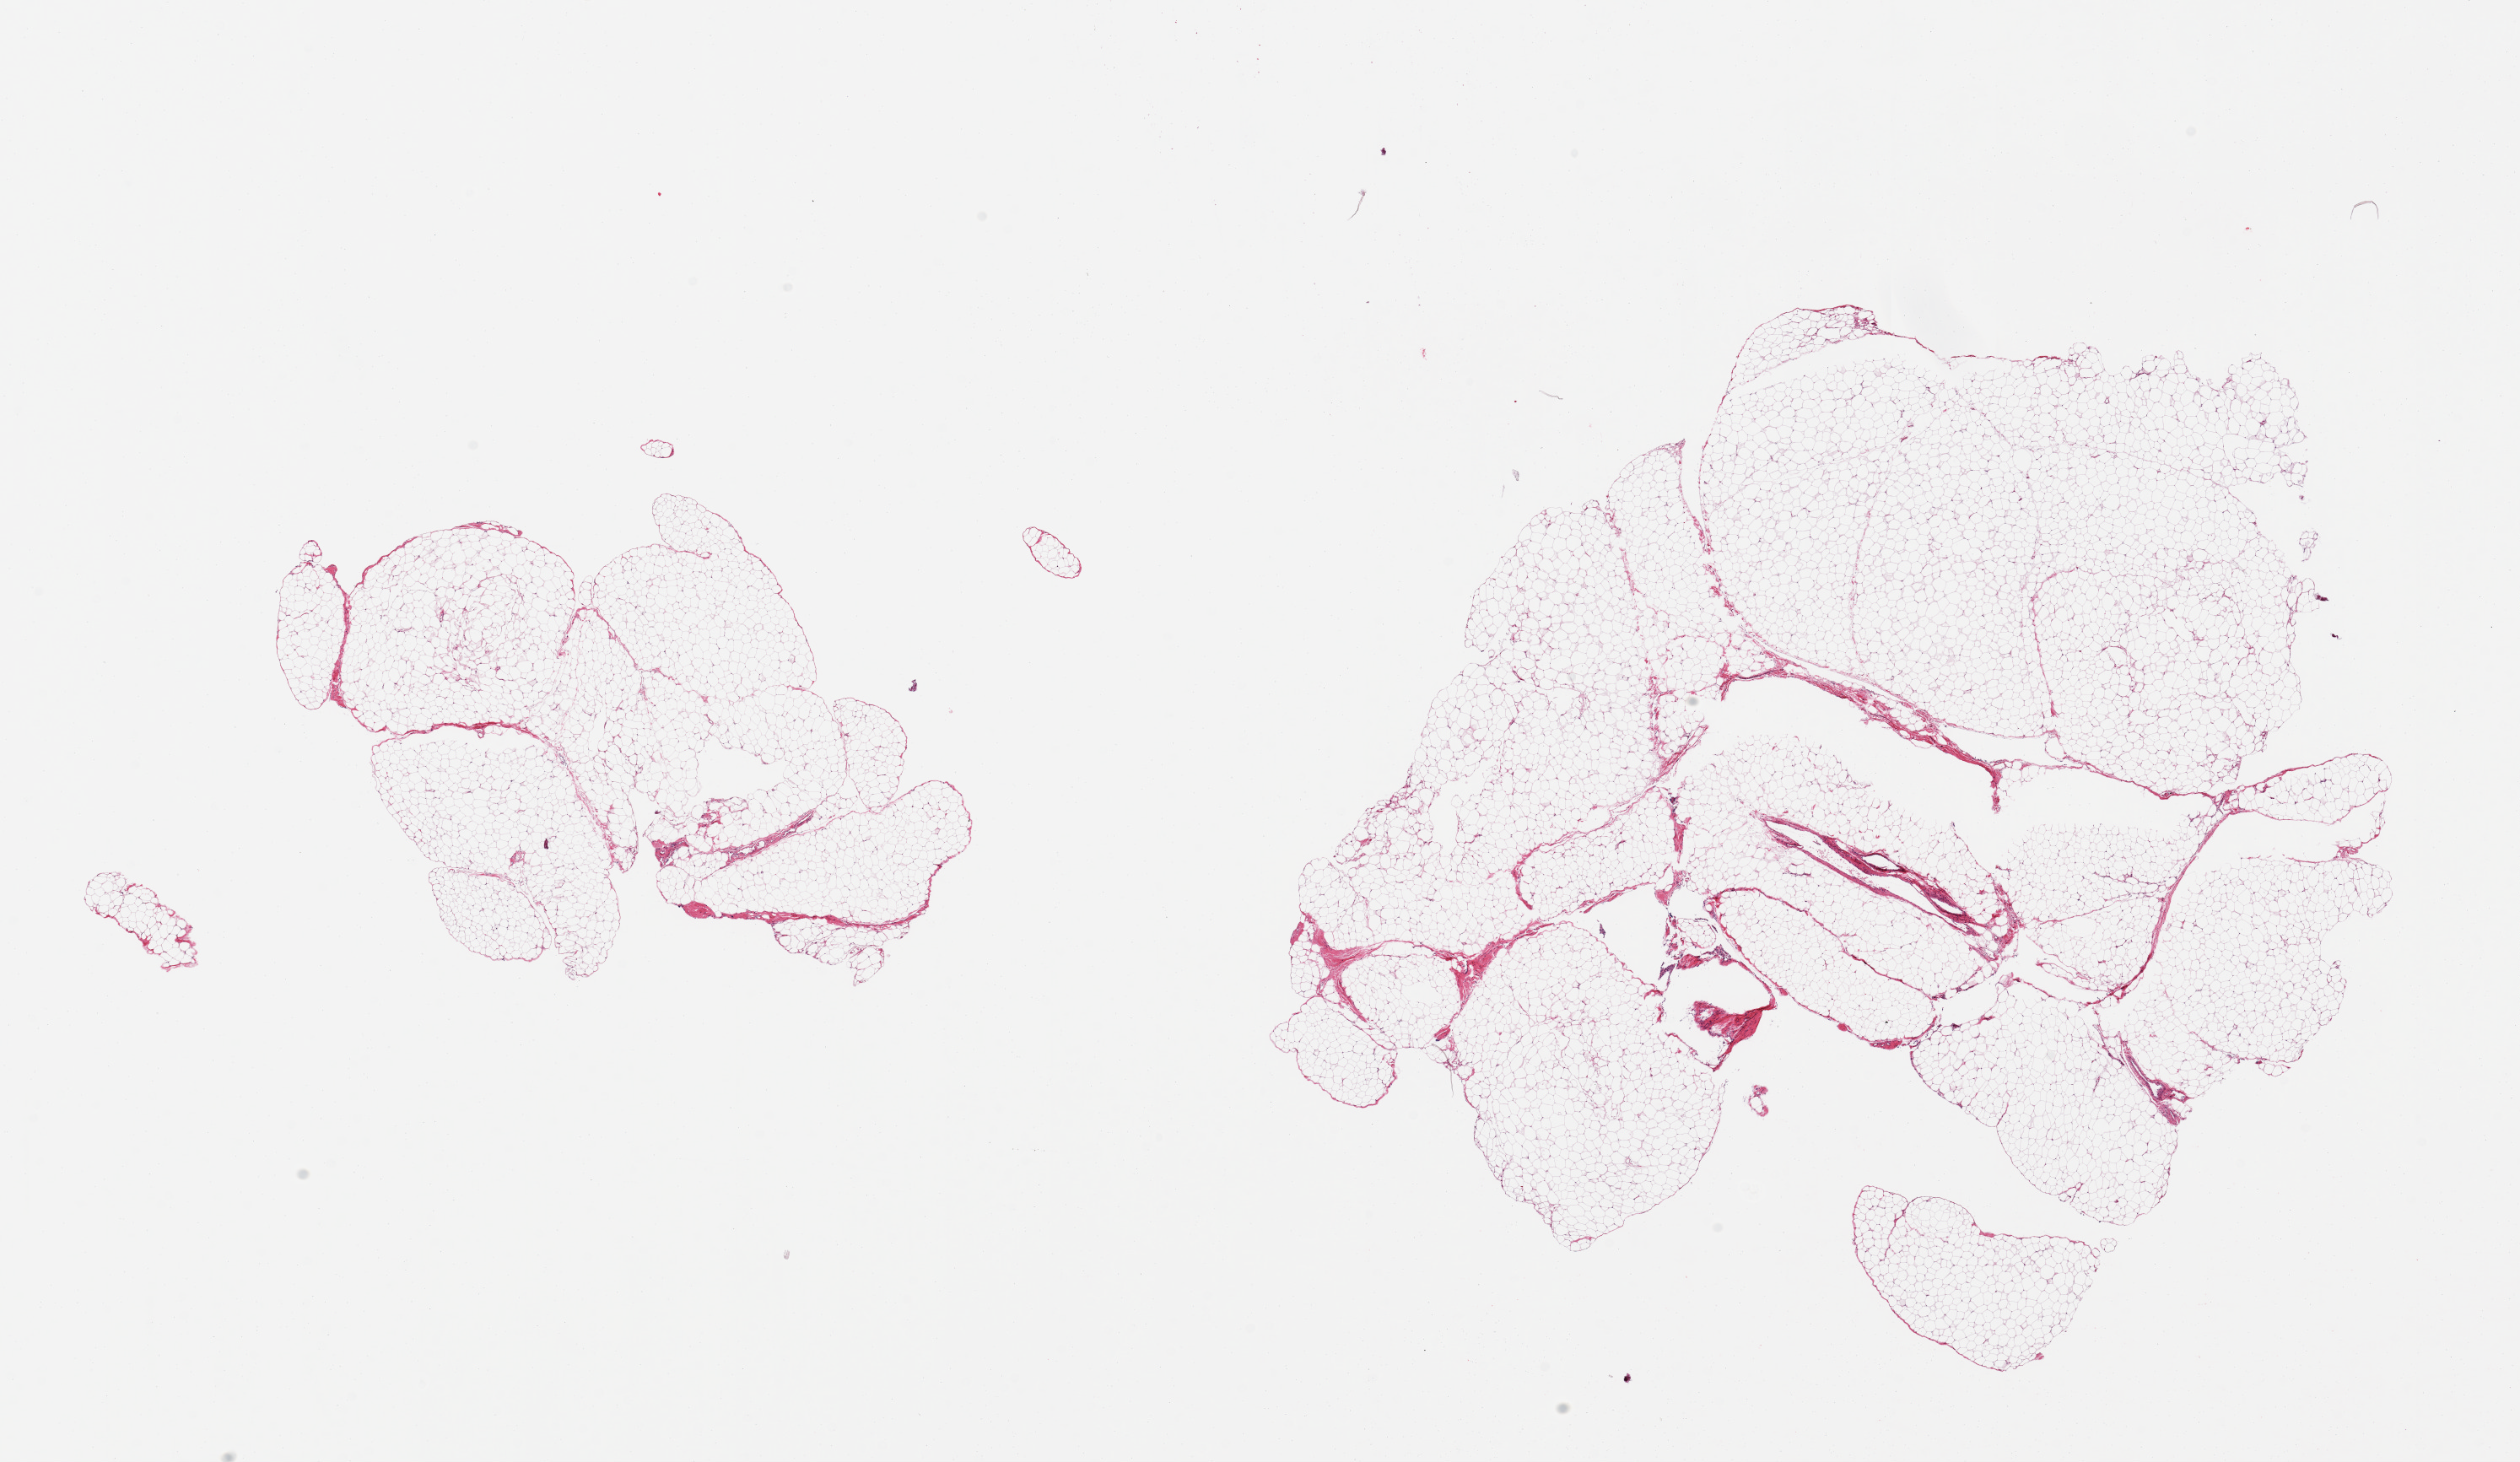
Digitized hematoxylin and eosin (H&E)-stained section — low-resolution overview of the scanned area, about 23.6 x 13.7 mm, PAXgene-fixed paraffin-embedded (PFPE) section, target tissue: omentum, tissue donor sample.
Reviewer comment on this tissue sample: 2 pieces; mature fat.